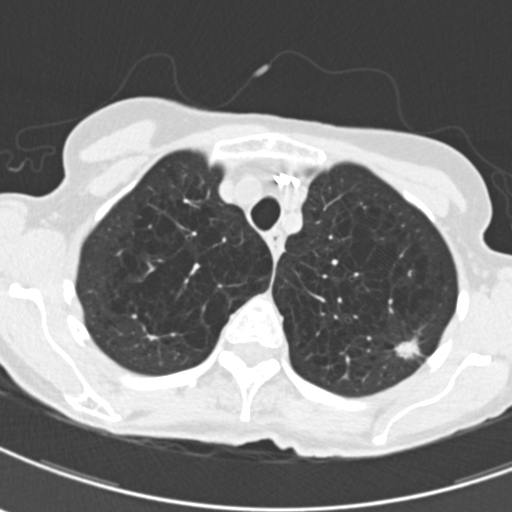
Low-dose screening chest CT, one axial slice; slice 162 of 203 in the series (ordered by position); reconstruction kernel B30f; 120 kVp; lung window (W 1500 / L -600 HU); 2 mm slice thickness; 512 × 512 image matrix, field of view 279 × 279 mm.
Annotated regions visible in this slice (manually delineated by an expert):
- lesion 1 (tumor, upper lobe of left lung): bounding box [x1, y1, x2, y2] px = [395, 337, 422, 359]